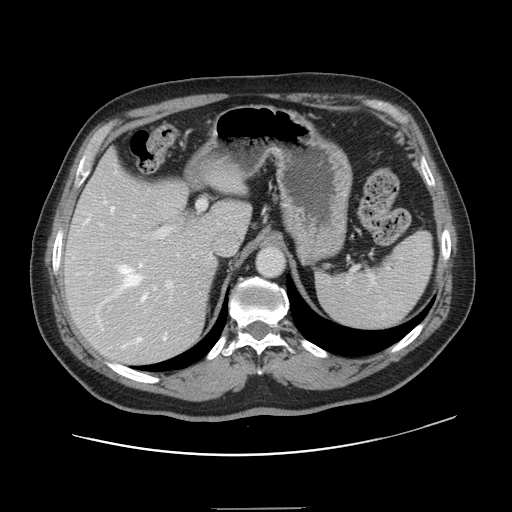
Contrast-enhanced abdominal CT, one axial slice; position 97 of 143 along the scan axis; 120 kVp; intravenous contrast given; soft-tissue window (W 400 / L 40 HU); 512 × 512 image matrix, field of view 402 × 402 mm. Male patient, age 62 years. Case-level facts recorded for this patient, not image findings: diagnosis: colorectal cancer liver metastases, imaged before liver resection; multiple liver metastases: yes; largest metastasis: 2.7 cm; disease in both lobes: no.
Outlined on this slice (manually delineated by an expert):
- hepatic veins: bounding box (x1, y1, x2, y2) in pixels: (86, 201, 179, 347)
- liver: (66, 154, 249, 363)
- planned liver remnant (the part of the liver to remain after resection): (67, 154, 250, 258)
- portal vein (with intrahepatic branches): (100, 201, 206, 289)